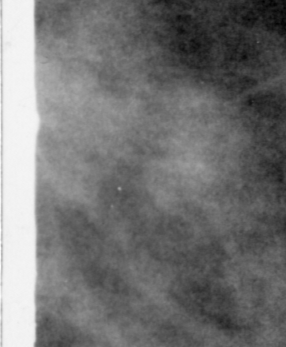
Crop from a digitized film mammogram around one marked abnormality, right breast, CC view.
Mass, shape irregular, margins ill defined; BI-RADS assessment category 4; pathology (as recorded): benign.